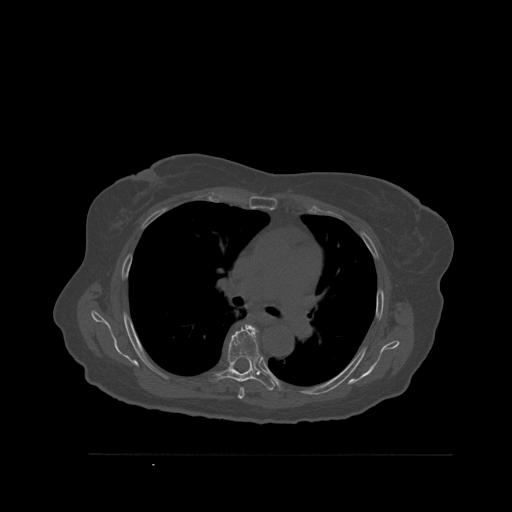
CT including the spine, one axial slice; slice 383 of 527 in the series (ordered by position); bone window (W 1800 / L 400 HU); 512 × 512 image matrix, field of view 470 × 470 mm. Patient: female, 73 years. Case-level facts recorded for this patient, not image findings: primary cancer: breast; vertebrae with lytic lesions (as recorded): L2.
Outlined on this slice (semi-automatically segmented with operator editing):
- T5 vertebra: bounding box (x1, y1, x2, y2) in pixels: (238, 388, 245, 399)
- T6 vertebra: (209, 325, 276, 391)